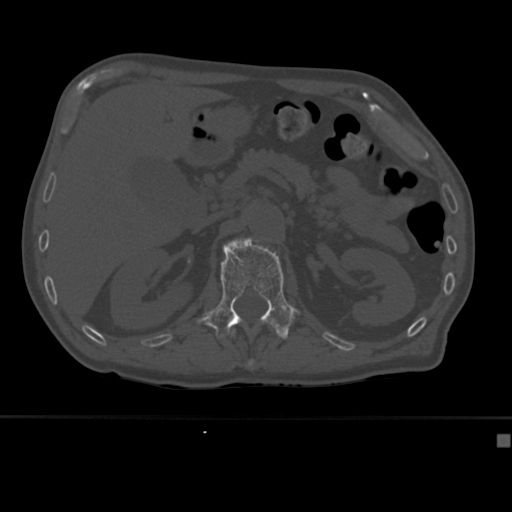
CT including the spine, one axial slice; position 173 of 430 along the scan axis; 120 kVp; bone window (W 1800 / L 400 HU); 1.5 mm slice thickness; 512 × 512 image matrix. Patient: male, 64 years. Case-level facts recorded for this patient, not image findings: primary cancer: uterus; vertebrae with lytic lesions (as recorded): T1, T4, T5, T7, L5.
Annotated regions visible in this slice (semi-automatic segmentation, software-assisted and operator-edited):
- L1 vertebra: bounding box (x1, y1, x2, y2) in pixels: (197, 238, 299, 340)
- T12 vertebra: (231, 329, 254, 368)